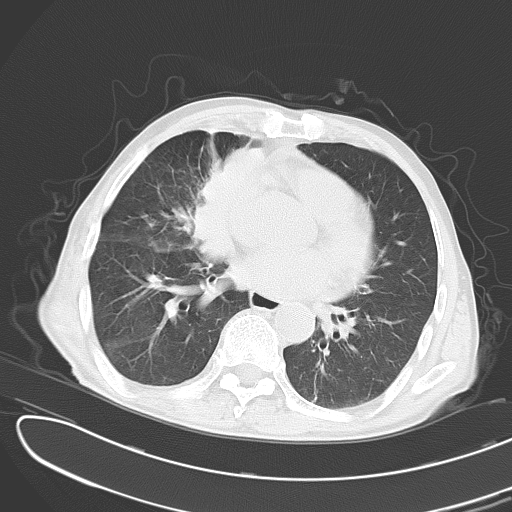
Chest CT, one axial slice. Slice 13 of 43 in the series (ordered by position). Reconstruction kernel B70f. 120 kVp. Lung window (W 1500 / L -600 HU). 512 × 512 image matrix, field of view 353 × 353 mm. Male patient, age 65 years. Case-level facts recorded for this patient, not image findings: clinical TNM (as recorded): T2 N3 M1.
Structures marked on this image (rectangle marked by the reading radiologist):
- lung tumour (recorded histology: small cell carcinoma): bounding box (x1, y1, x2, y2) in pixels: (194, 136, 271, 269)